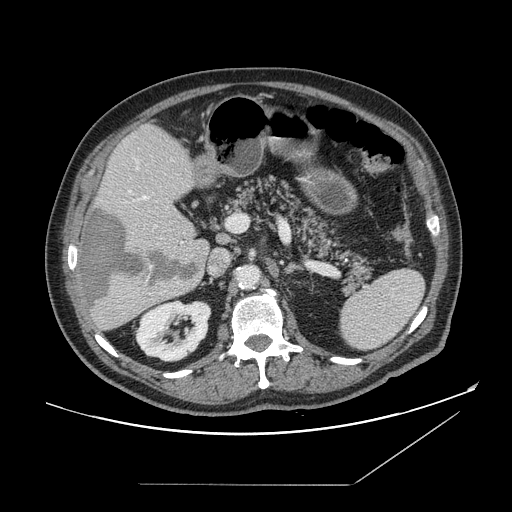
Contrast-enhanced abdominal CT, one axial slice; slice 85 of 166 in the series (ordered by position); 120 kVp; soft-tissue window (W 400 / L 40 HU); 2.5 mm slice thickness; 512 × 512 image matrix, field of view 416 × 416 mm. Male patient, age 80 years. From the clinical record (not read from this slice): diagnosis: colorectal cancer liver metastases, imaged before liver resection; multiple liver metastases: no; largest metastasis: 2.2 cm.
Annotated regions visible in this slice (outlined manually by an expert reader):
- hepatic veins: bounding box (x1, y1, x2, y2) in pixels: (137, 168, 147, 200)
- liver: (78, 126, 209, 331)
- planned liver remnant (the part of the liver to remain after resection): (100, 126, 198, 237)
- portal vein (with intrahepatic branches): (130, 191, 231, 244)
- liver metastasis: (82, 209, 199, 309)